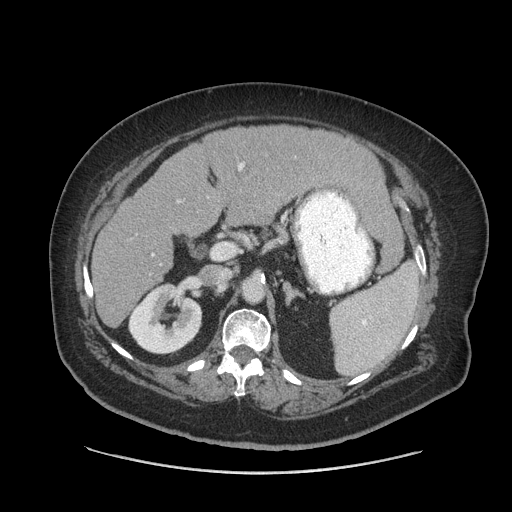
Contrast-enhanced abdominal CT (liver protocol), one axial slice. Slice 42 of 91 in the series (ordered by position). Reconstruction kernel STANDARD. Soft-tissue window (W 400 / L 40 HU). 2.5 mm slice thickness. 512 × 512 image matrix, field of view 420 × 420 mm. From the clinical record (not read from this slice): diagnosis: hepatocellular carcinoma (patient treated with transarterial chemoembolisation; whether this scan precedes or follows treatment is not stated here); TNM stage (as recorded): Stage-I; Child-Pugh class: A; tumour differentiation: well differentiated; tumour nodularity: uninodular.
Outlined on this slice (semi-automatic segmentation, software-assisted and operator-edited):
- liver parenchyma outside the tumour (the mass and vessels are separate outlines, so this box may not span the whole liver): bounding box [x1, y1, x2, y2] px = [92, 126, 388, 326]
- liver vessels: [152, 163, 244, 256]